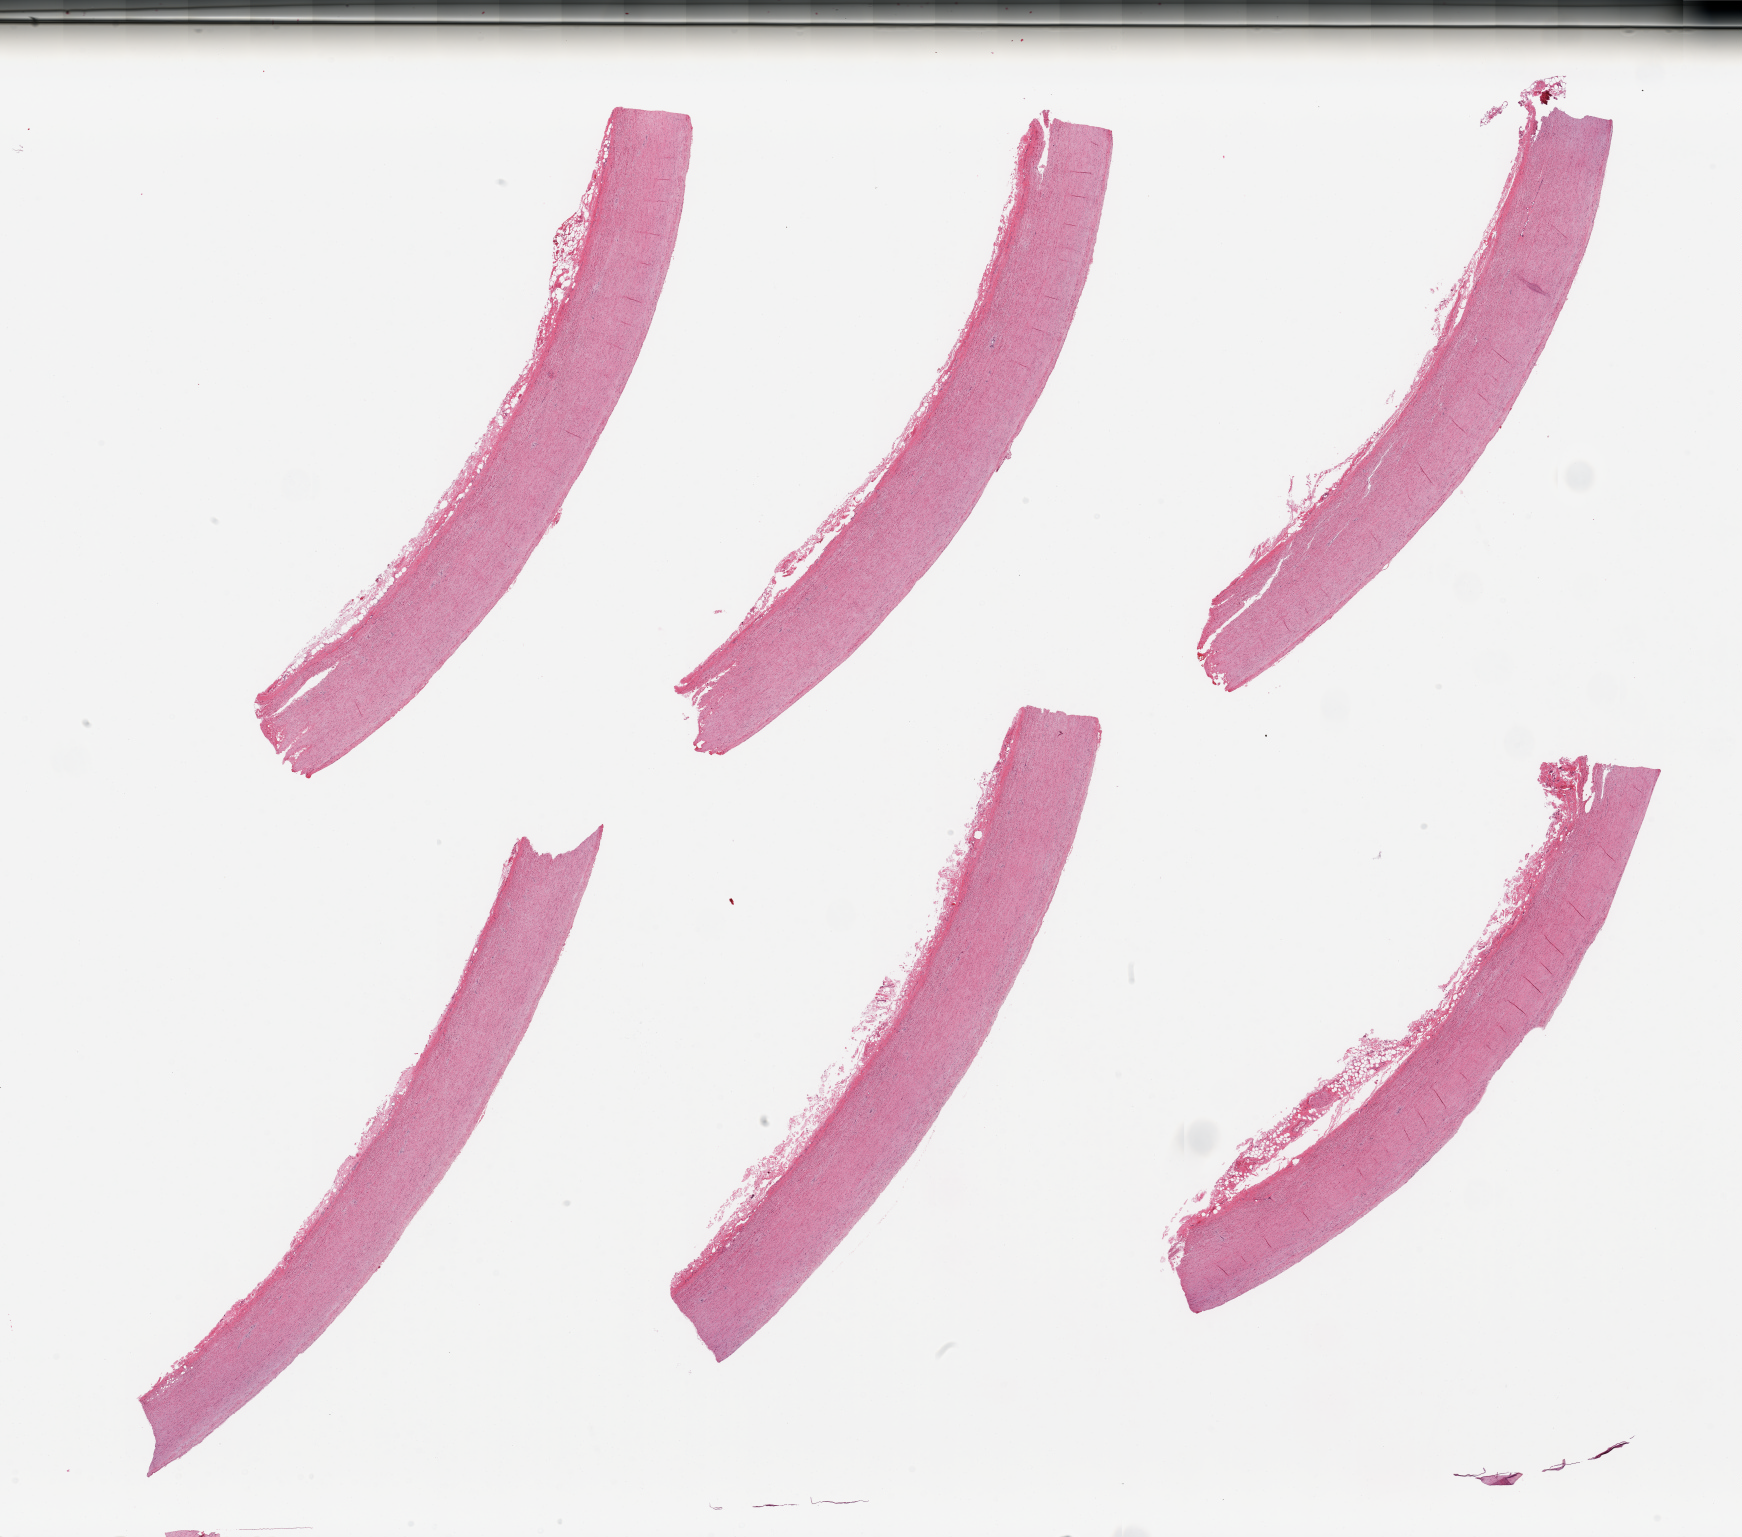
Haematoxylin and eosin whole-slide image — shown as a low-resolution overview of the whole scanned area (about 27.6 x 24.3 mm, acquisition: 20x scan), PAXgene-fixed, paraffin-embedded tissue, target tissue: aorta, donor tissue sample.
- review note (as recorded): 6 pieces, minimal atherosis